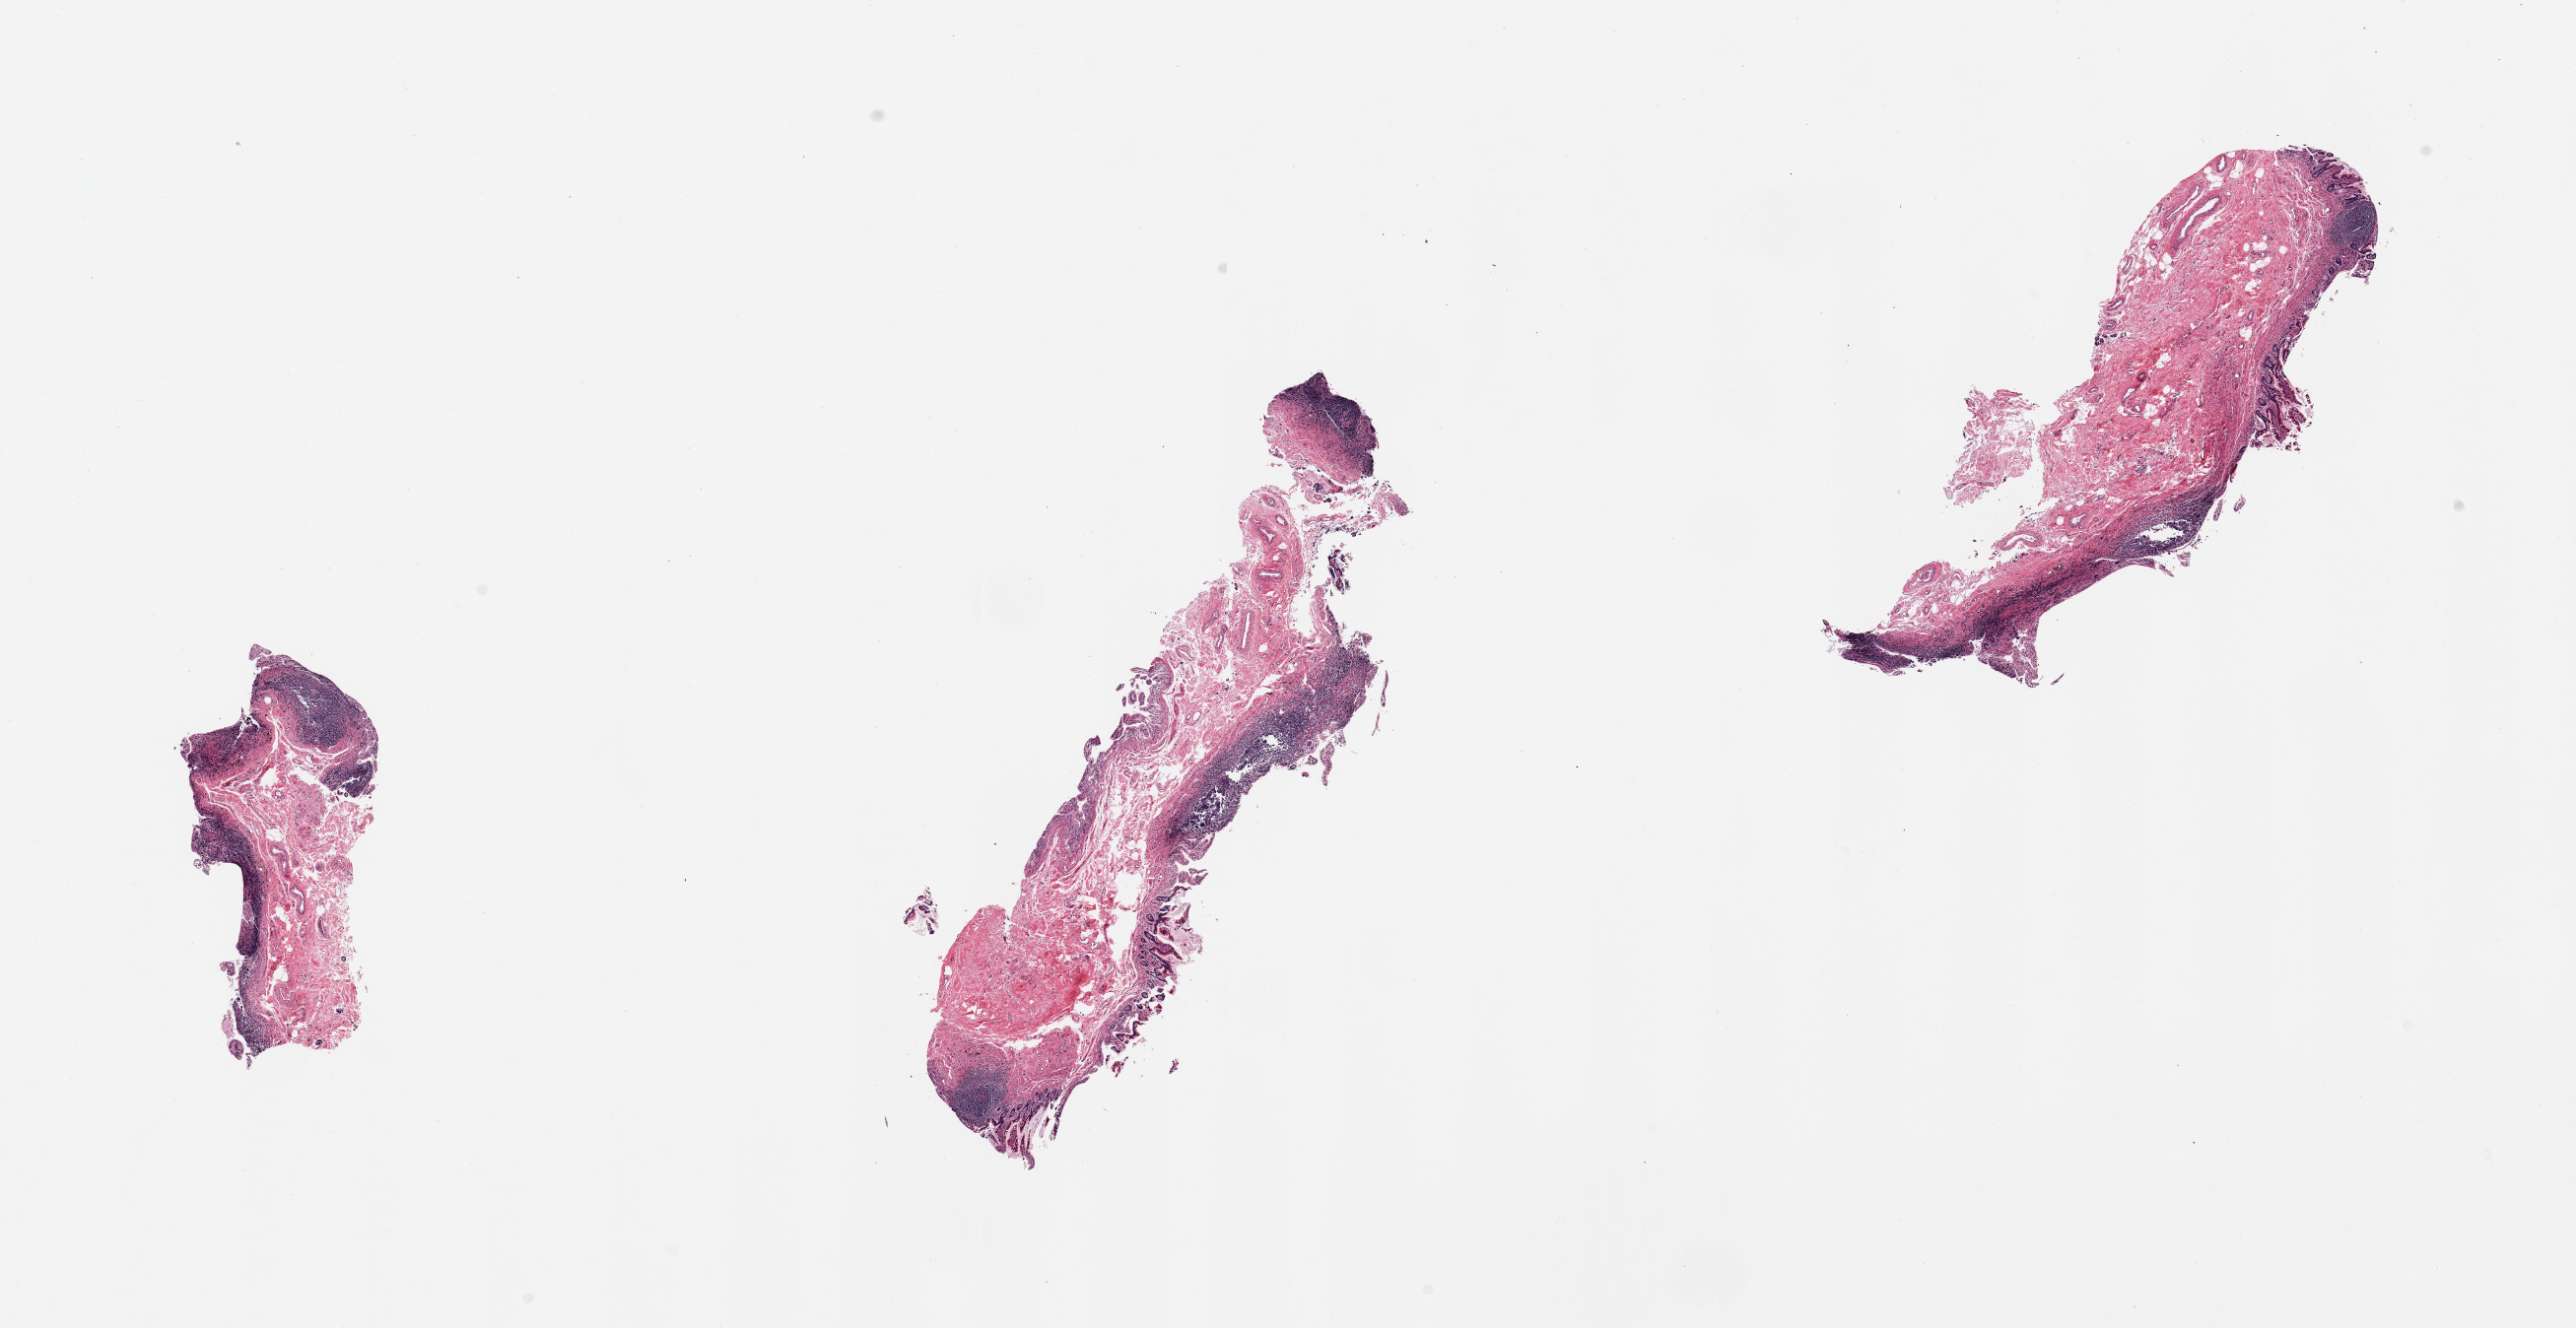
Haematoxylin and eosin whole-slide image — low-resolution overview of the scanned area, about 20.7 x 10.7 mm; PAXgene-fixed, paraffin-embedded tissue; section of ileum (target tissue); donor tissue sample. Donor: female.
Reviewer comment on this tissue sample: 3 pieces; variably autolyzed mucosa with focally prominent lymphoid component.